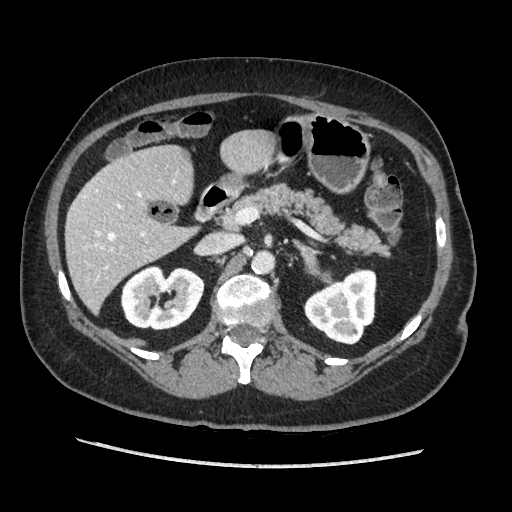
Contrast-enhanced abdominal CT, one axial slice; position 110 of 203 along the scan axis; soft-tissue window (W 400 / L 40 HU); 512 × 512 image matrix, field of view 360 × 360 mm. Female patient. From the clinical record (not read from this slice): diagnosis: adrenocortical carcinoma; tumour side: left adrenal; tumour size at pathology: 6.5 cm; Ki-67 index: 22 %.
Annotated regions visible in this slice (semi-automatic segmentation, software-assisted and operator-edited):
- mass: bounding box [x1, y1, x2, y2] px = [303, 248, 318, 271]